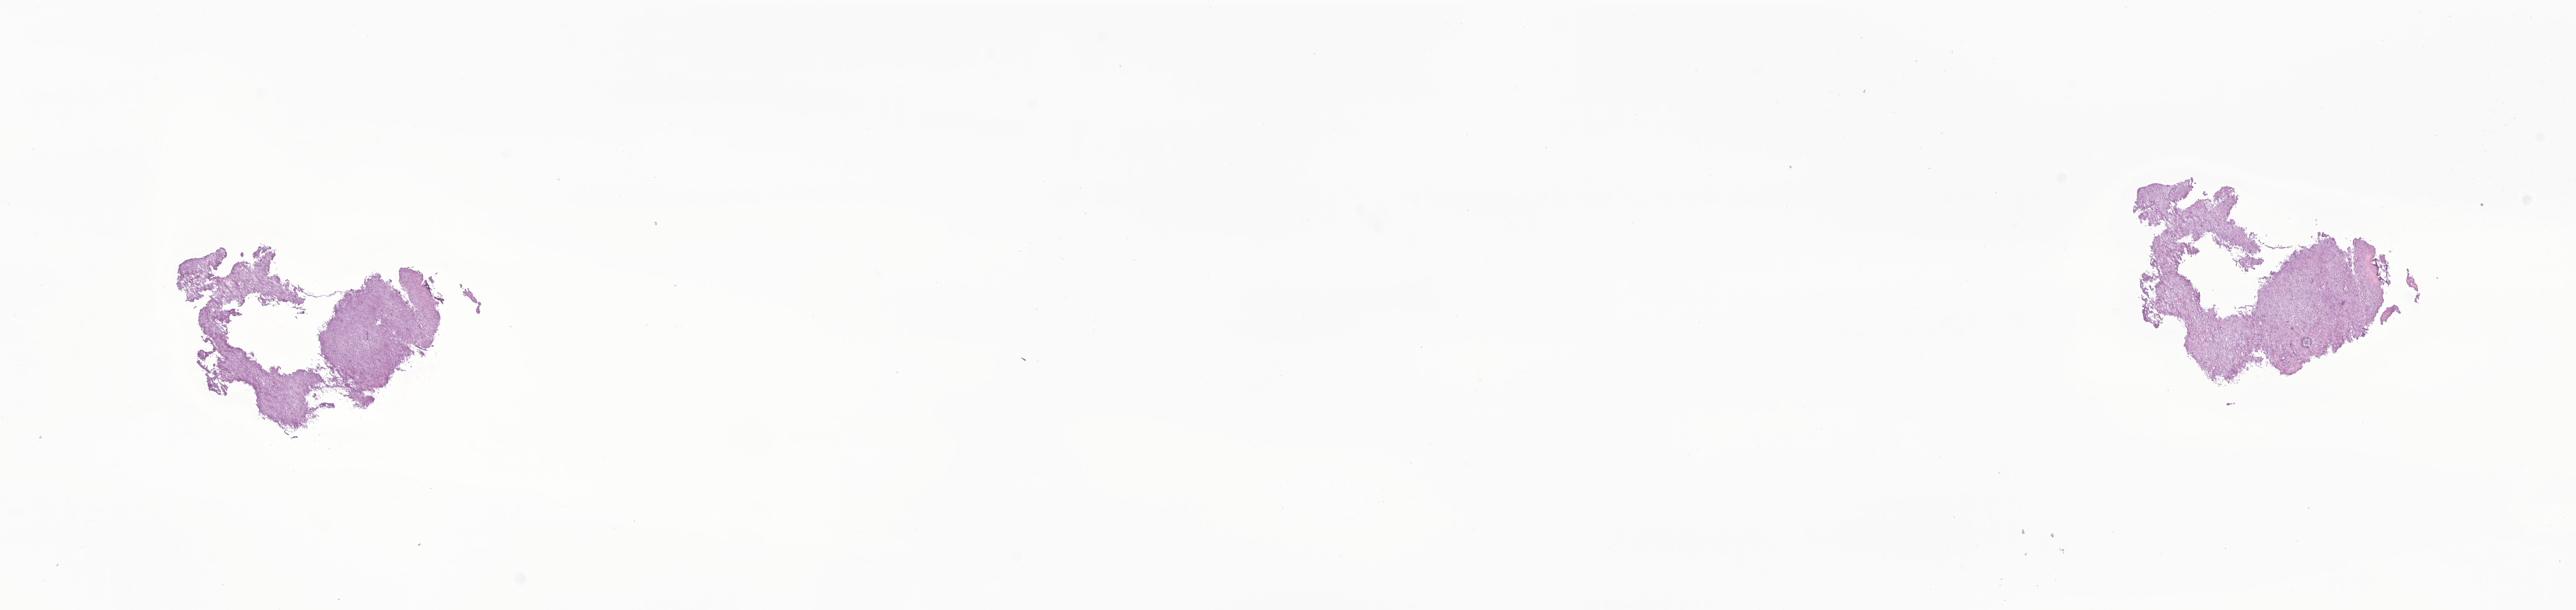
Digitized haematoxylin and eosin-stained section of tumor tissue from the brain — low-resolution overview of the scanned area, about 26.8 x 6.4 mm; cryosection (OCT / tissue freezing medium). Patient: male, age 141 months (11 years 9 months).
• diagnosis (ICD-O-3 morphology term): Neoplasm, malignant